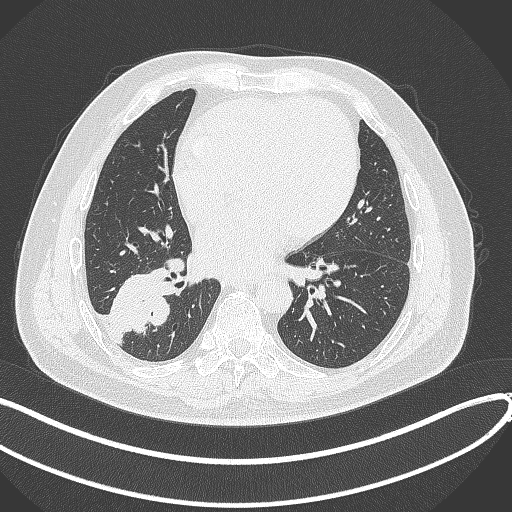
Chest CT, one axial slice; slice 151 of 360 in the series (ordered by position); 120 kVp; lung window (W 1500 / L -600 HU); 512 × 512 image matrix, field of view 400 × 400 mm. Male patient, age 59 years.
Outlined on this slice (rectangle marked by the reading radiologist):
- lung tumour (recorded histology: adenocarcinoma): bounding box <109,258,168,338> (left, top, right, bottom; pixels)